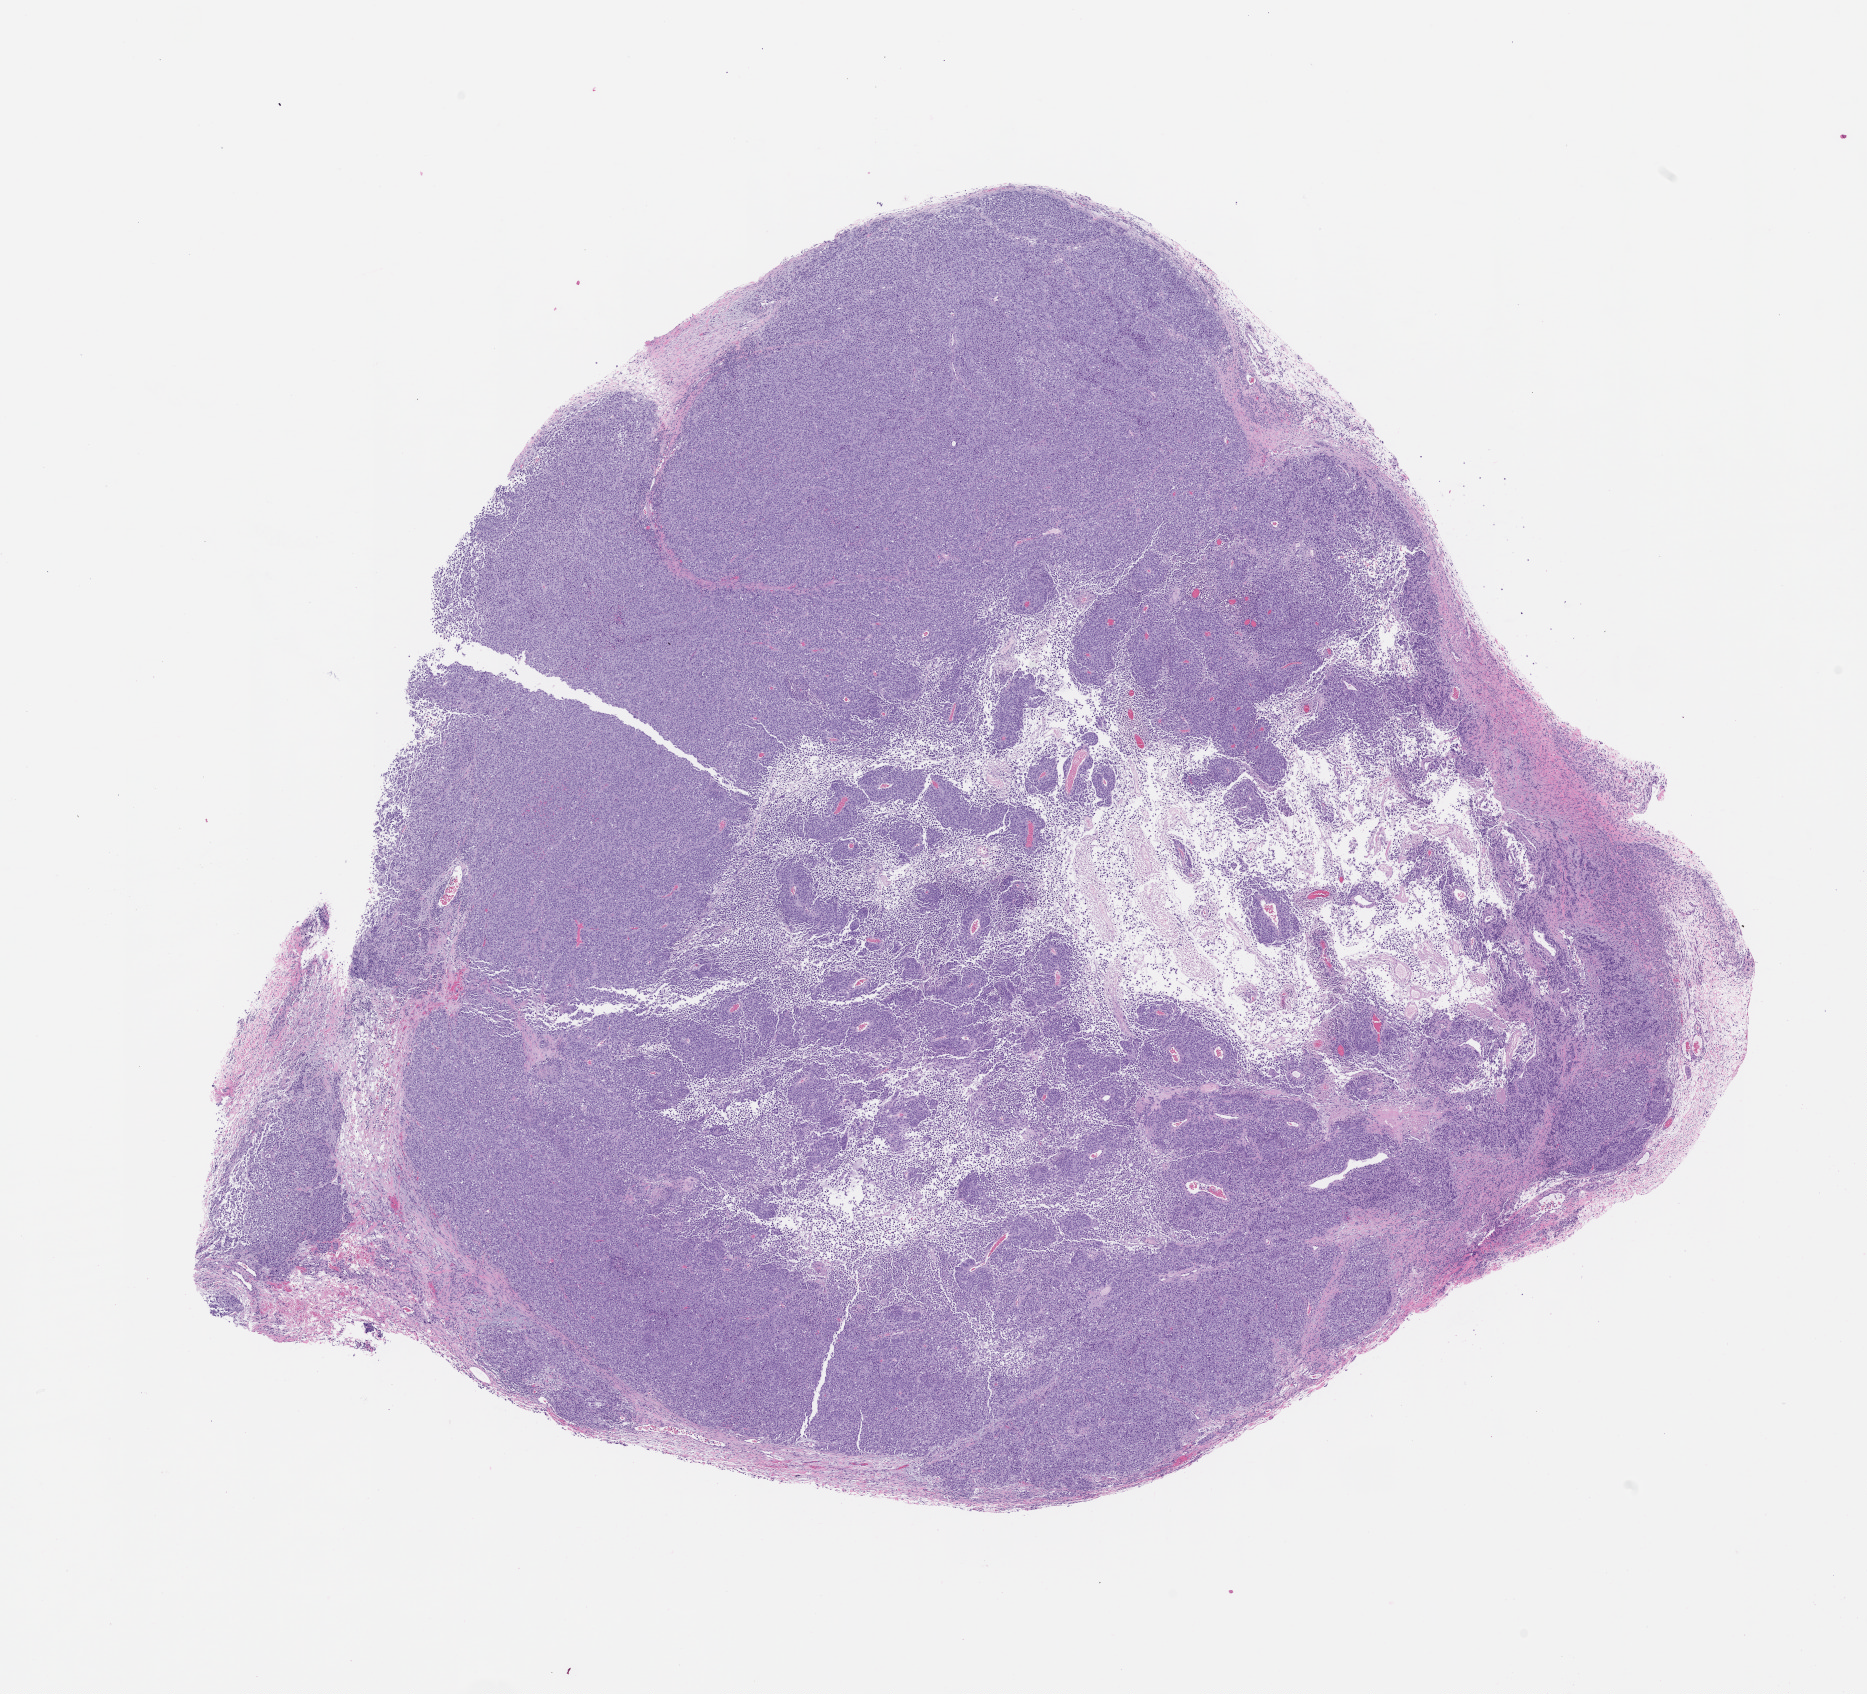
Whole-slide image, H&E: patient-derived xenograft (human tumor grown in a mouse), passage 3 — low-resolution overview of the scanned area, about 15.0 x 13.6 mm; FFPE section; originating tumor site category: skin.
Originating patient diagnosis: Melanoma.